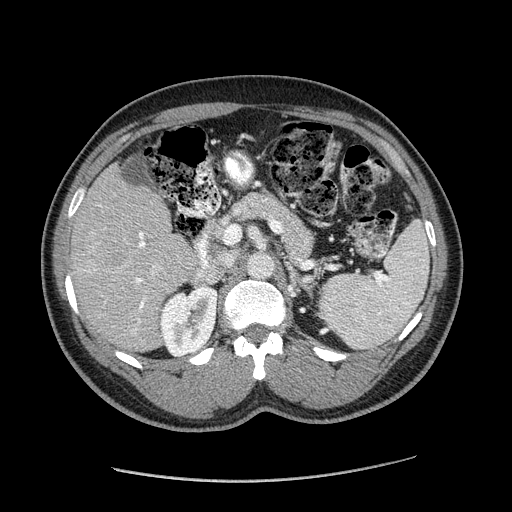
Contrast-enhanced abdominal CT (liver protocol), one axial slice; slice 95 of 182 in the series (ordered by position); soft-tissue window (W 400 / L 40 HU); 2.5 mm slice thickness; 512 × 512 image matrix. Case-level facts recorded for this patient, not image findings: diagnosis: hepatocellular carcinoma (patient treated with transarterial chemoembolisation; whether this scan precedes or follows treatment is not stated here); TNM stage (as recorded): Stage-I; Child-Pugh class: A; tumour differentiation: well differentiated; tumour nodularity: uninodular.
Annotated regions visible in this slice (semi-automatically segmented with operator editing):
- liver parenchyma outside the tumour (the mass and vessels are separate outlines, so this box may not span the whole liver): box from (x=70, y=164) to (x=204, y=352) px
- mass: (x=91, y=234)–(x=134, y=274)
- liver vessels: (x=88, y=205)–(x=202, y=331)